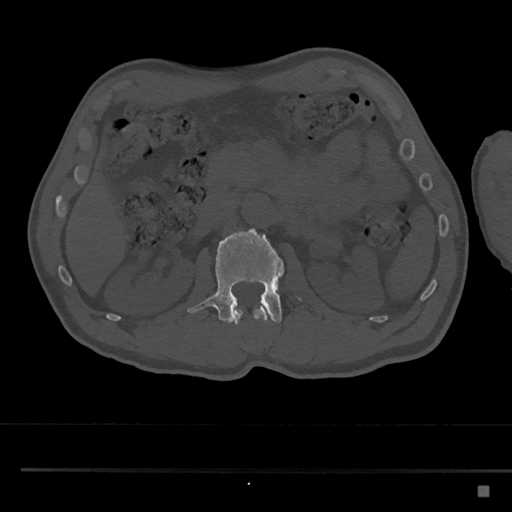
CT including the spine, one axial slice; slice 779 of 797 in the series (ordered by position); 120 kVp; bone window (W 1800 / L 400 HU); 0.5 mm slice thickness; 512 × 512 image matrix, field of view 391 × 391 mm. Male patient, age 59 years. From the clinical record (not read from this slice): primary cancer: prostate.
Structures marked on this image (semi-automatic segmentation, software-assisted and operator-edited):
- L1 vertebra: bounding box (x1, y1, x2, y2) in pixels: (232, 306, 270, 324)
- L2 vertebra: (187, 228, 303, 323)